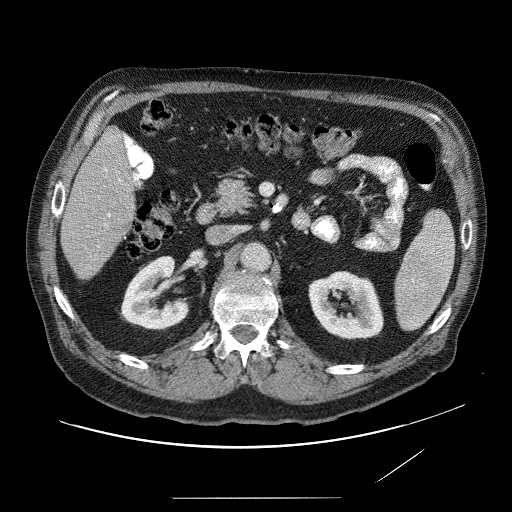
Contrast-enhanced abdominal CT (liver protocol), one axial slice; position 23 of 89 along the scan axis; soft-tissue window (W 400 / L 40 HU); 512 × 512 image matrix, field of view 420 × 420 mm. From the clinical record (not read from this slice): diagnosis: hepatocellular carcinoma (patient treated with transarterial chemoembolisation; whether this scan precedes or follows treatment is not stated here); TNM stage (as recorded): Stage-IVA; Child-Pugh class: A.
Outlined on this slice (semi-automatic segmentation, software-assisted and operator-edited):
- liver parenchyma outside the tumour (the mass and vessels are separate outlines, so this box may not span the whole liver): box from (x=60, y=121) to (x=142, y=284) px
- liver vessels: (x=107, y=180)–(x=129, y=236)